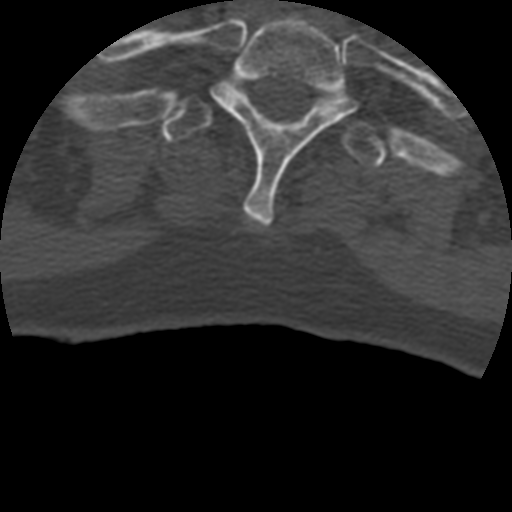
CT including the spine, one axial slice. Position 380 of 399 along the scan axis. Reconstruction kernel STANDARD. Bone window (W 1800 / L 400 HU). 1.25 mm slice thickness. 512 × 512 image matrix, field of view 160 × 160 mm. Patient age 69 years. From the clinical record (not read from this slice): primary cancer: prostate.
Structures marked on this image (semi-automatic segmentation, software-assisted and operator-edited):
- T1 vertebra: bounding box [x1, y1, x2, y2] px = [210, 16, 357, 228]
- T2 vertebra: [162, 81, 387, 168]